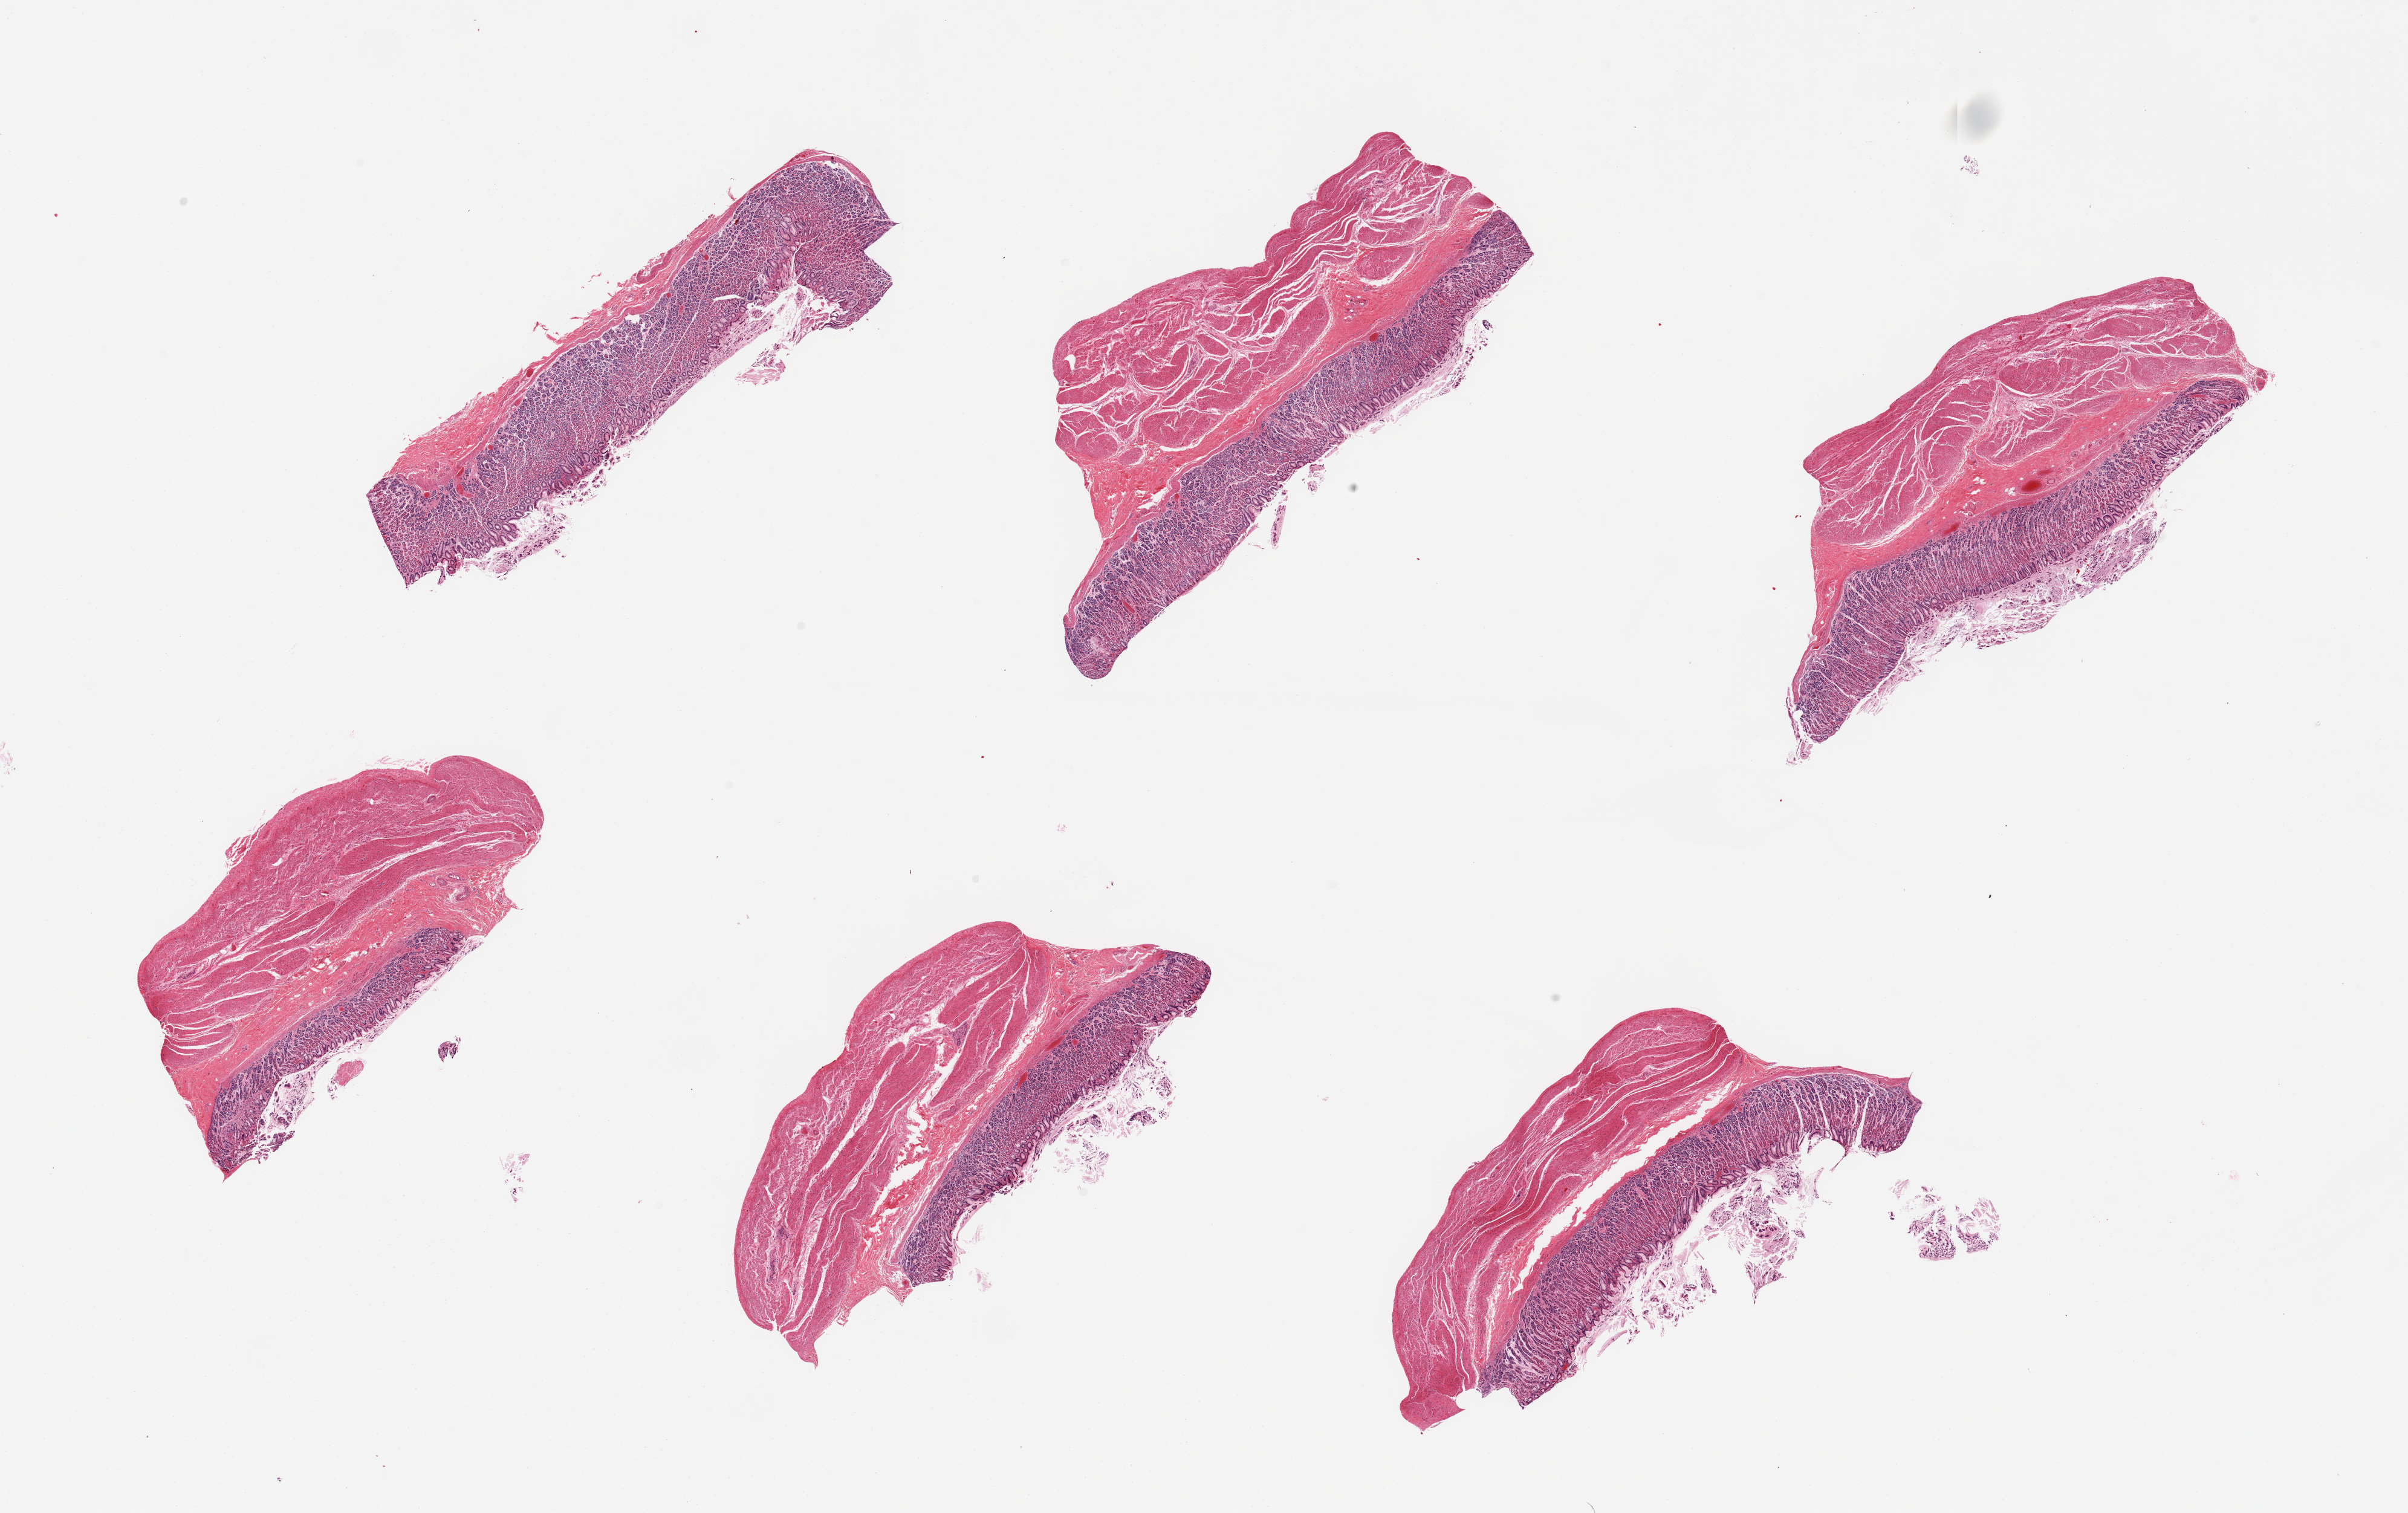
Digitized H&E-stained section, whole scanned area (about 31.5 x 19.8 mm, from a 20x scan) shown as a low-resolution overview; PAXgene-fixed, paraffin-embedded tissue; sampled site (target tissue): stomach; tissue donor sample. Donor: male.
Pathologist's review note for this sample: 6 pieces, mucosa well preserved, ~1mm thick, 30-50% thickness.